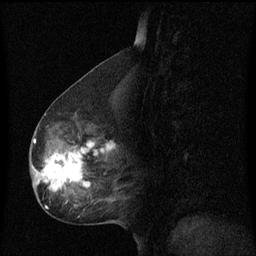
Breast MRI (dynamic contrast-enhanced), one sagittal slice. Position 32 of 60 along the scan axis. Dynamic contrast-enhanced series, image 2 of 3 at this slice position (ordered by acquisition). 1.5 T. TE 4.2 ms, TR 8.4 ms. 2 mm slice thickness. 256 × 256 image matrix. Patient: female, 49 years. From the clinical record (not read from this slice): setting: breast cancer imaged before/during neoadjuvant chemotherapy; receptor status: HR-positive, HER2-negative.
Structures marked on this image (semi-automatic segmentation, software-assisted and operator-edited):
- analysis volume of interest (the breast-tissue region the enhancement analysis was run in; not a lesion): bounding box <30,126,119,201> (left, top, right, bottom; pixels)
- tumour enhancement mask (voxels above the 70 % enhancement threshold inside the analysis volume of interest): <34,140,114,193>